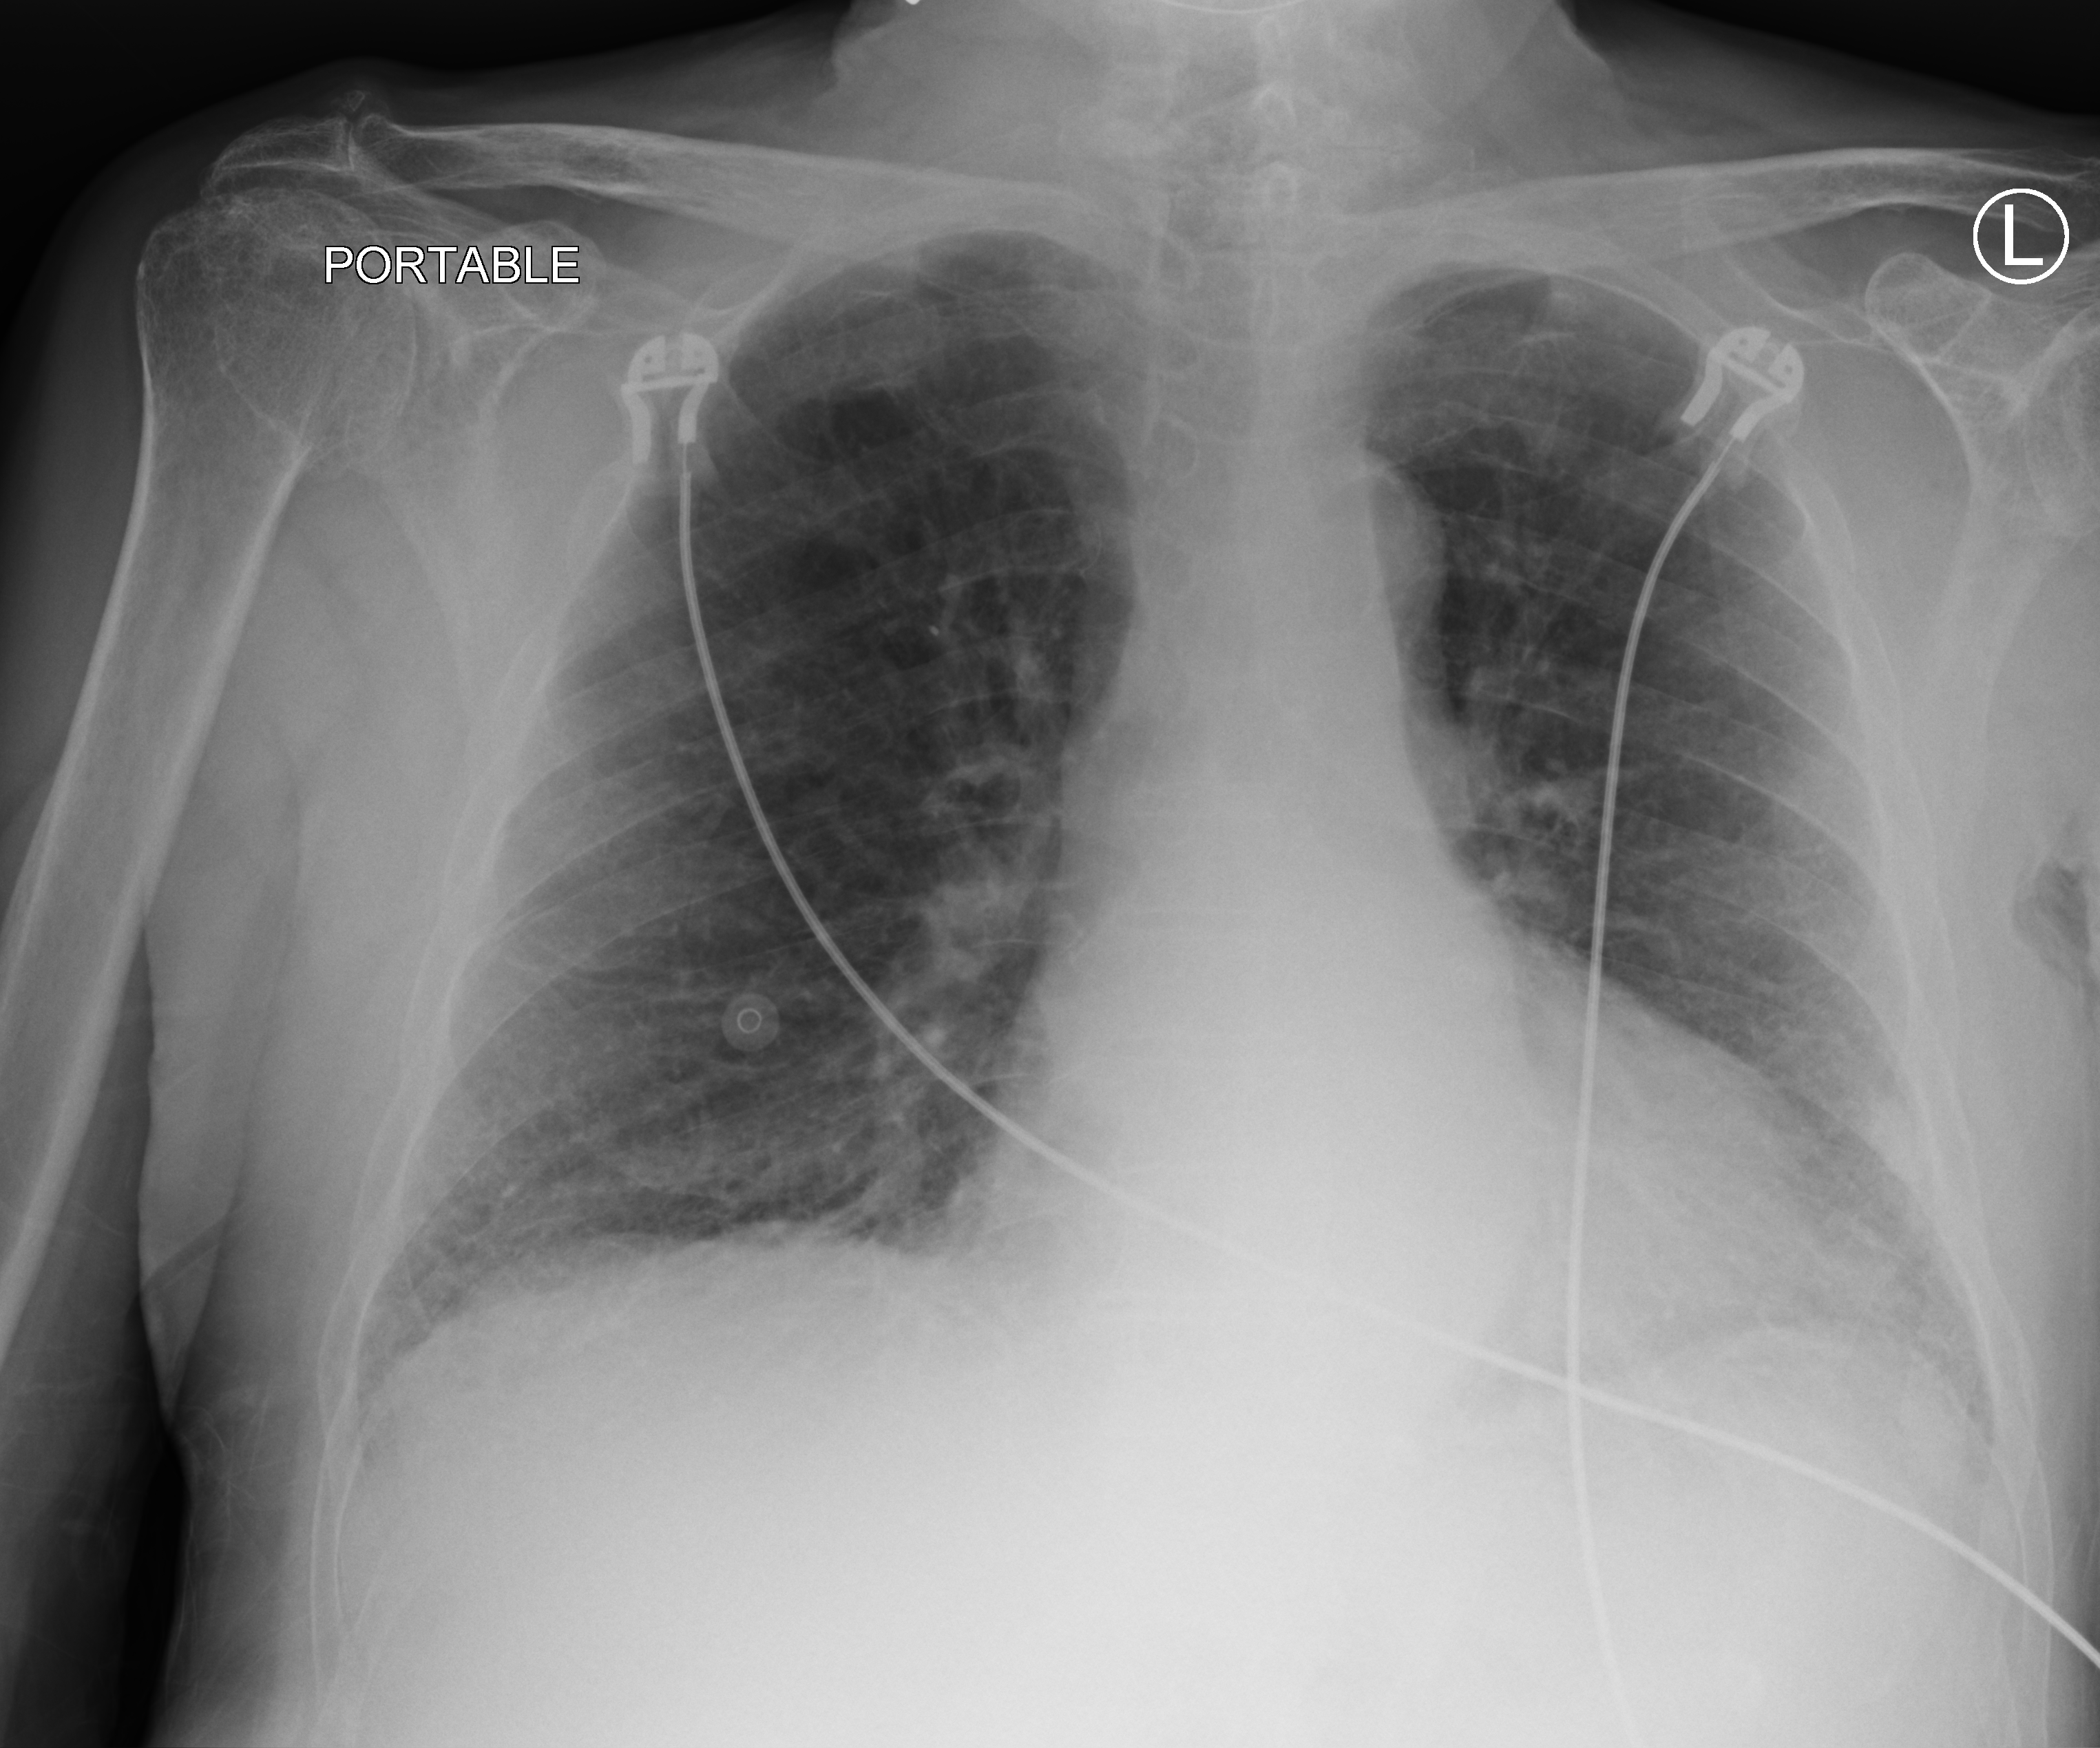
Portable chest radiograph; anteroposterior (AP) projection. Patient hospitalised with COVID-19; male, aged 75–90 years.
Admission-level facts for this patient (not findings on this image; timing relative to this image not recorded): mechanically ventilated during this hospital stay: no; smoking status (admission record): never; admitted to intensive care during this hospital stay: no.